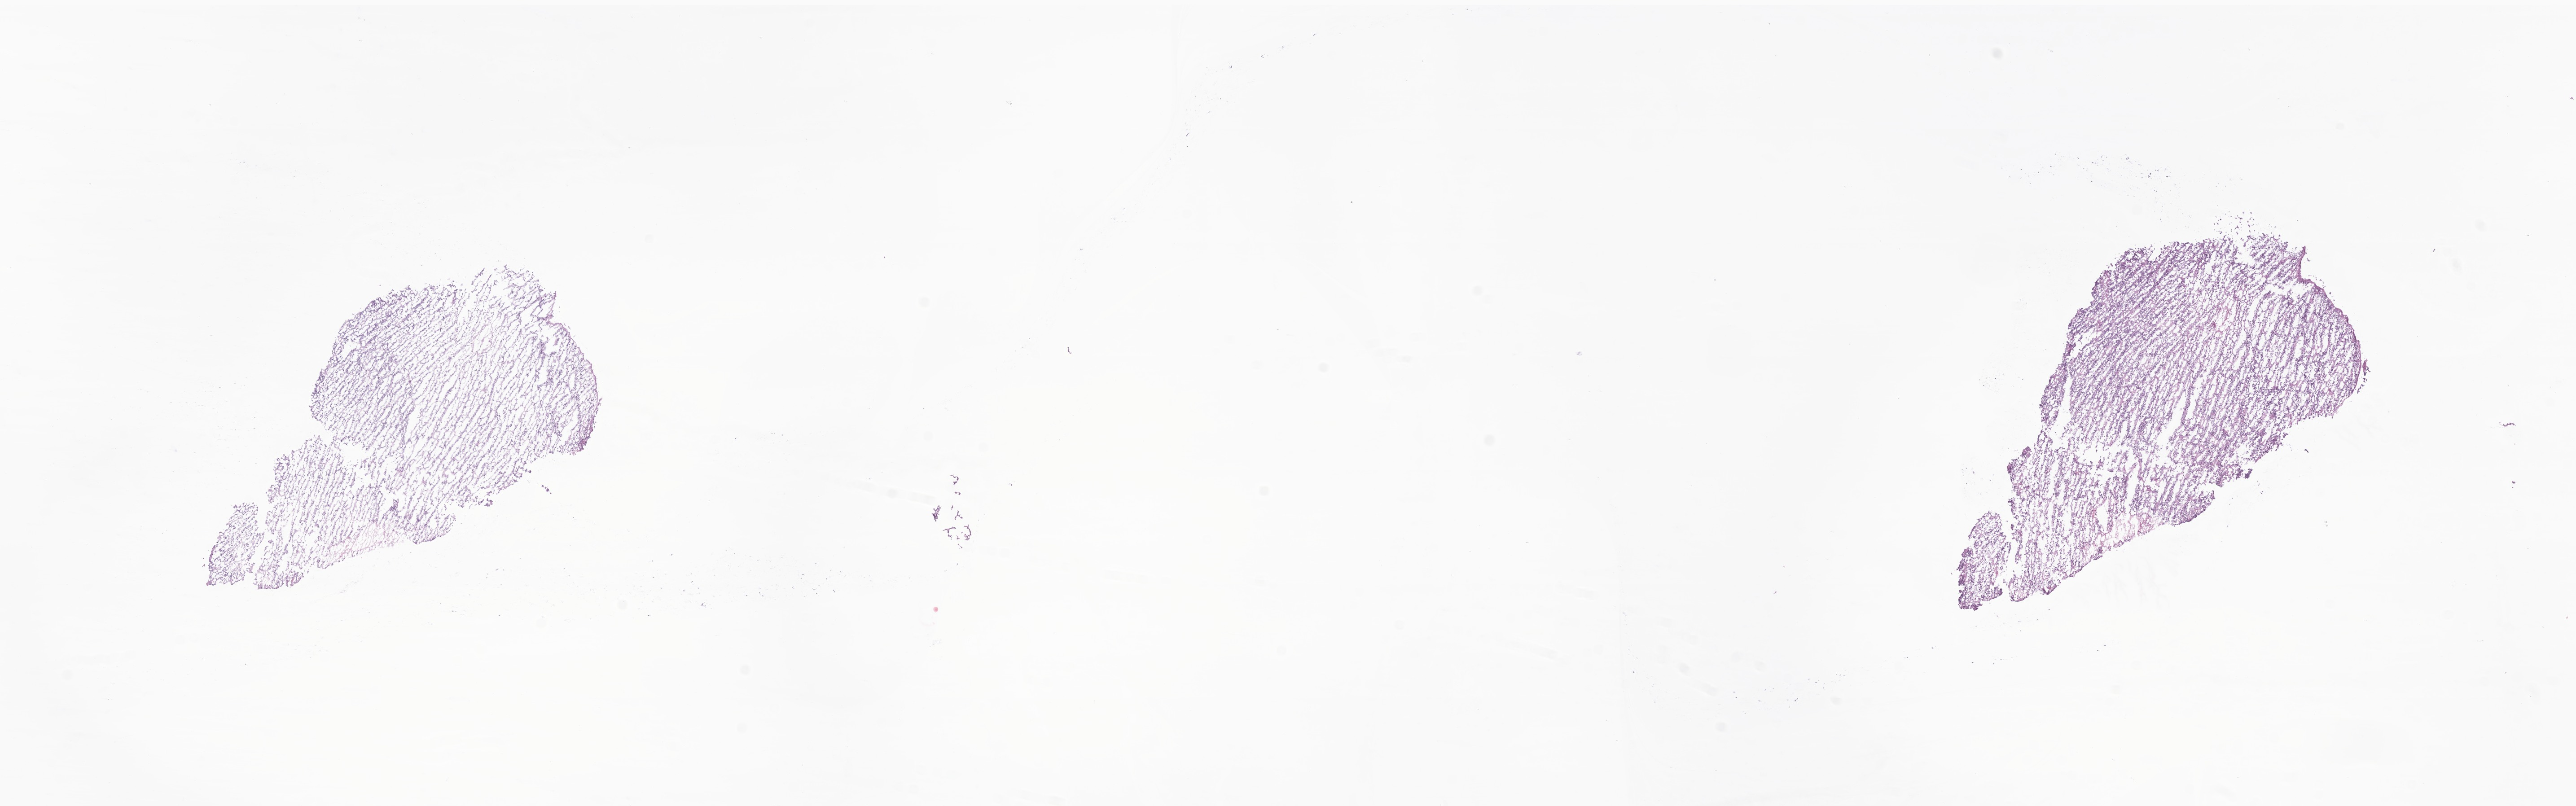
Whole-slide image, haematoxylin and eosin stain of tumor tissue from the brain, whole scanned area (about 24.2 x 7.6 mm) shown as a low-resolution overview, frozen section. Patient male; age 43 months (3 years 7 months).
Diagnosis: Neoplasm, uncertain whether benign or malignant.